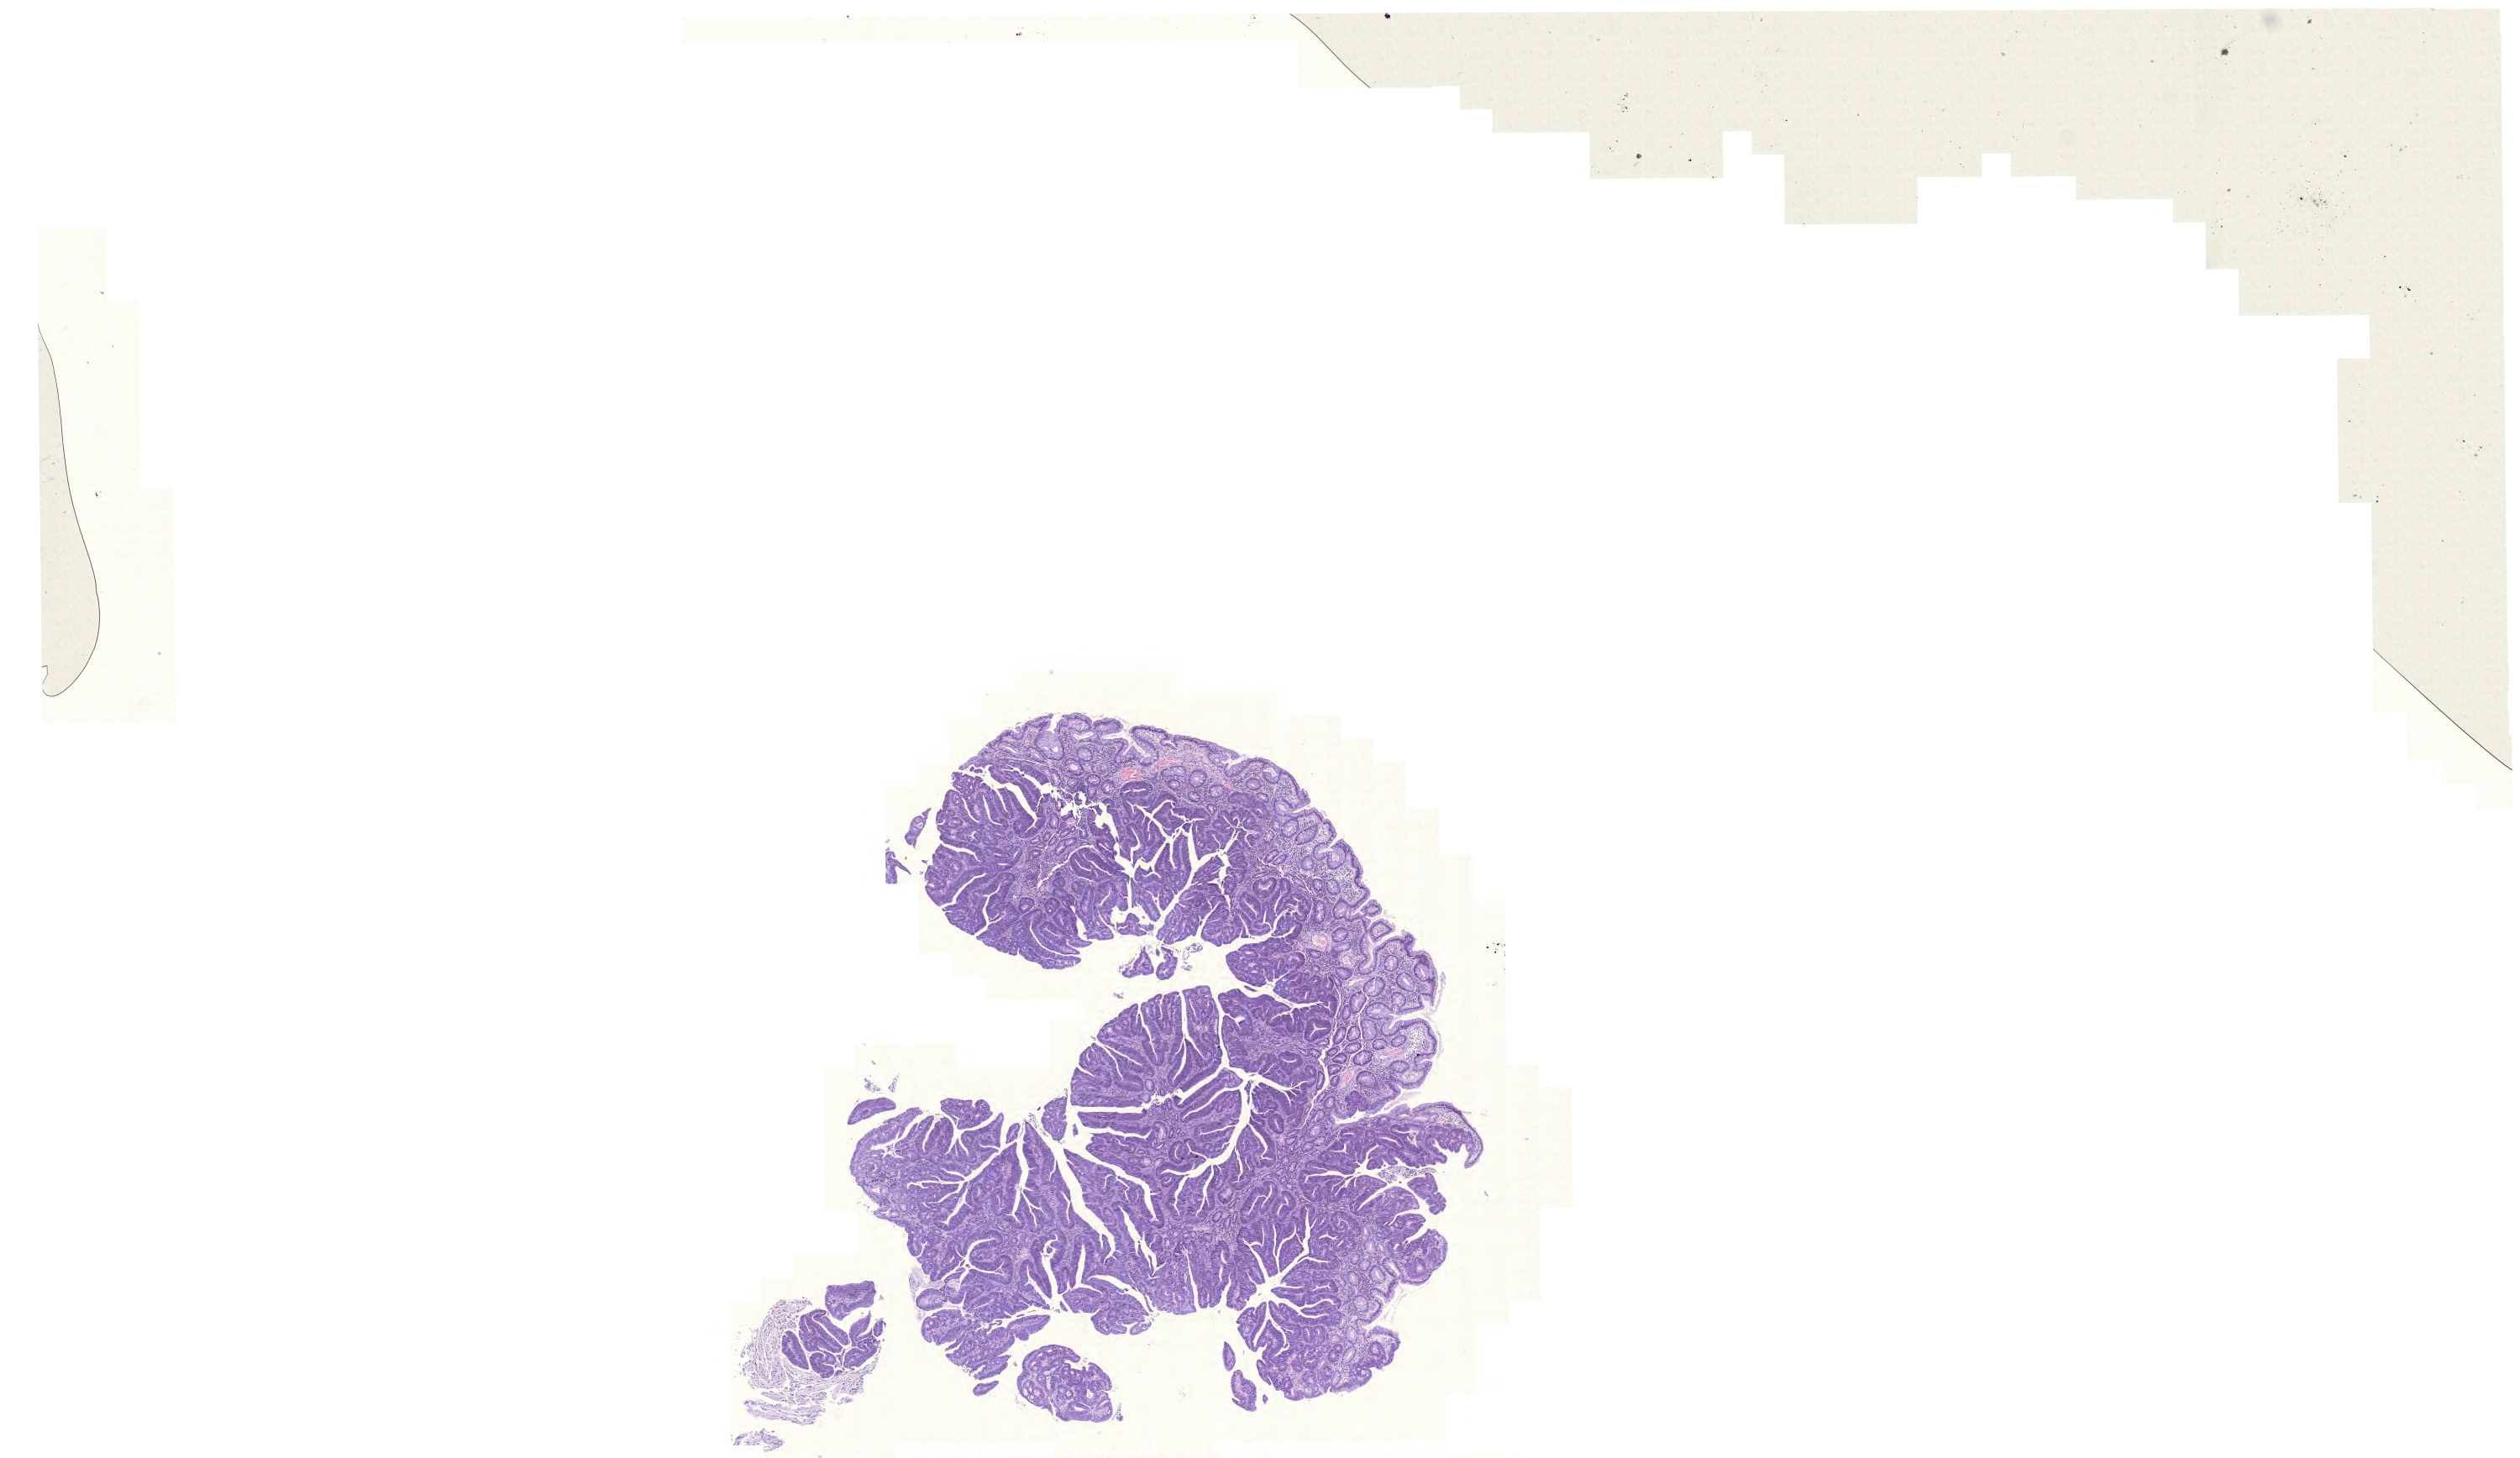
Whole-slide histology image, H&E-stained — shown as a low-resolution overview of the whole scanned area (about 22.3 x 12.9 mm), formalin-fixed paraffin-embedded (FFPE) diagnostic section, rectum, primary tumour sample. Patient: male, age at initial diagnosis 70 years.
Histologic diagnosis: Mucinous adenocarcinoma (rectosigmoid junction). Lymph nodes positive (case pathology): 0 of 12 examined. AJCC pathologic stage: I.